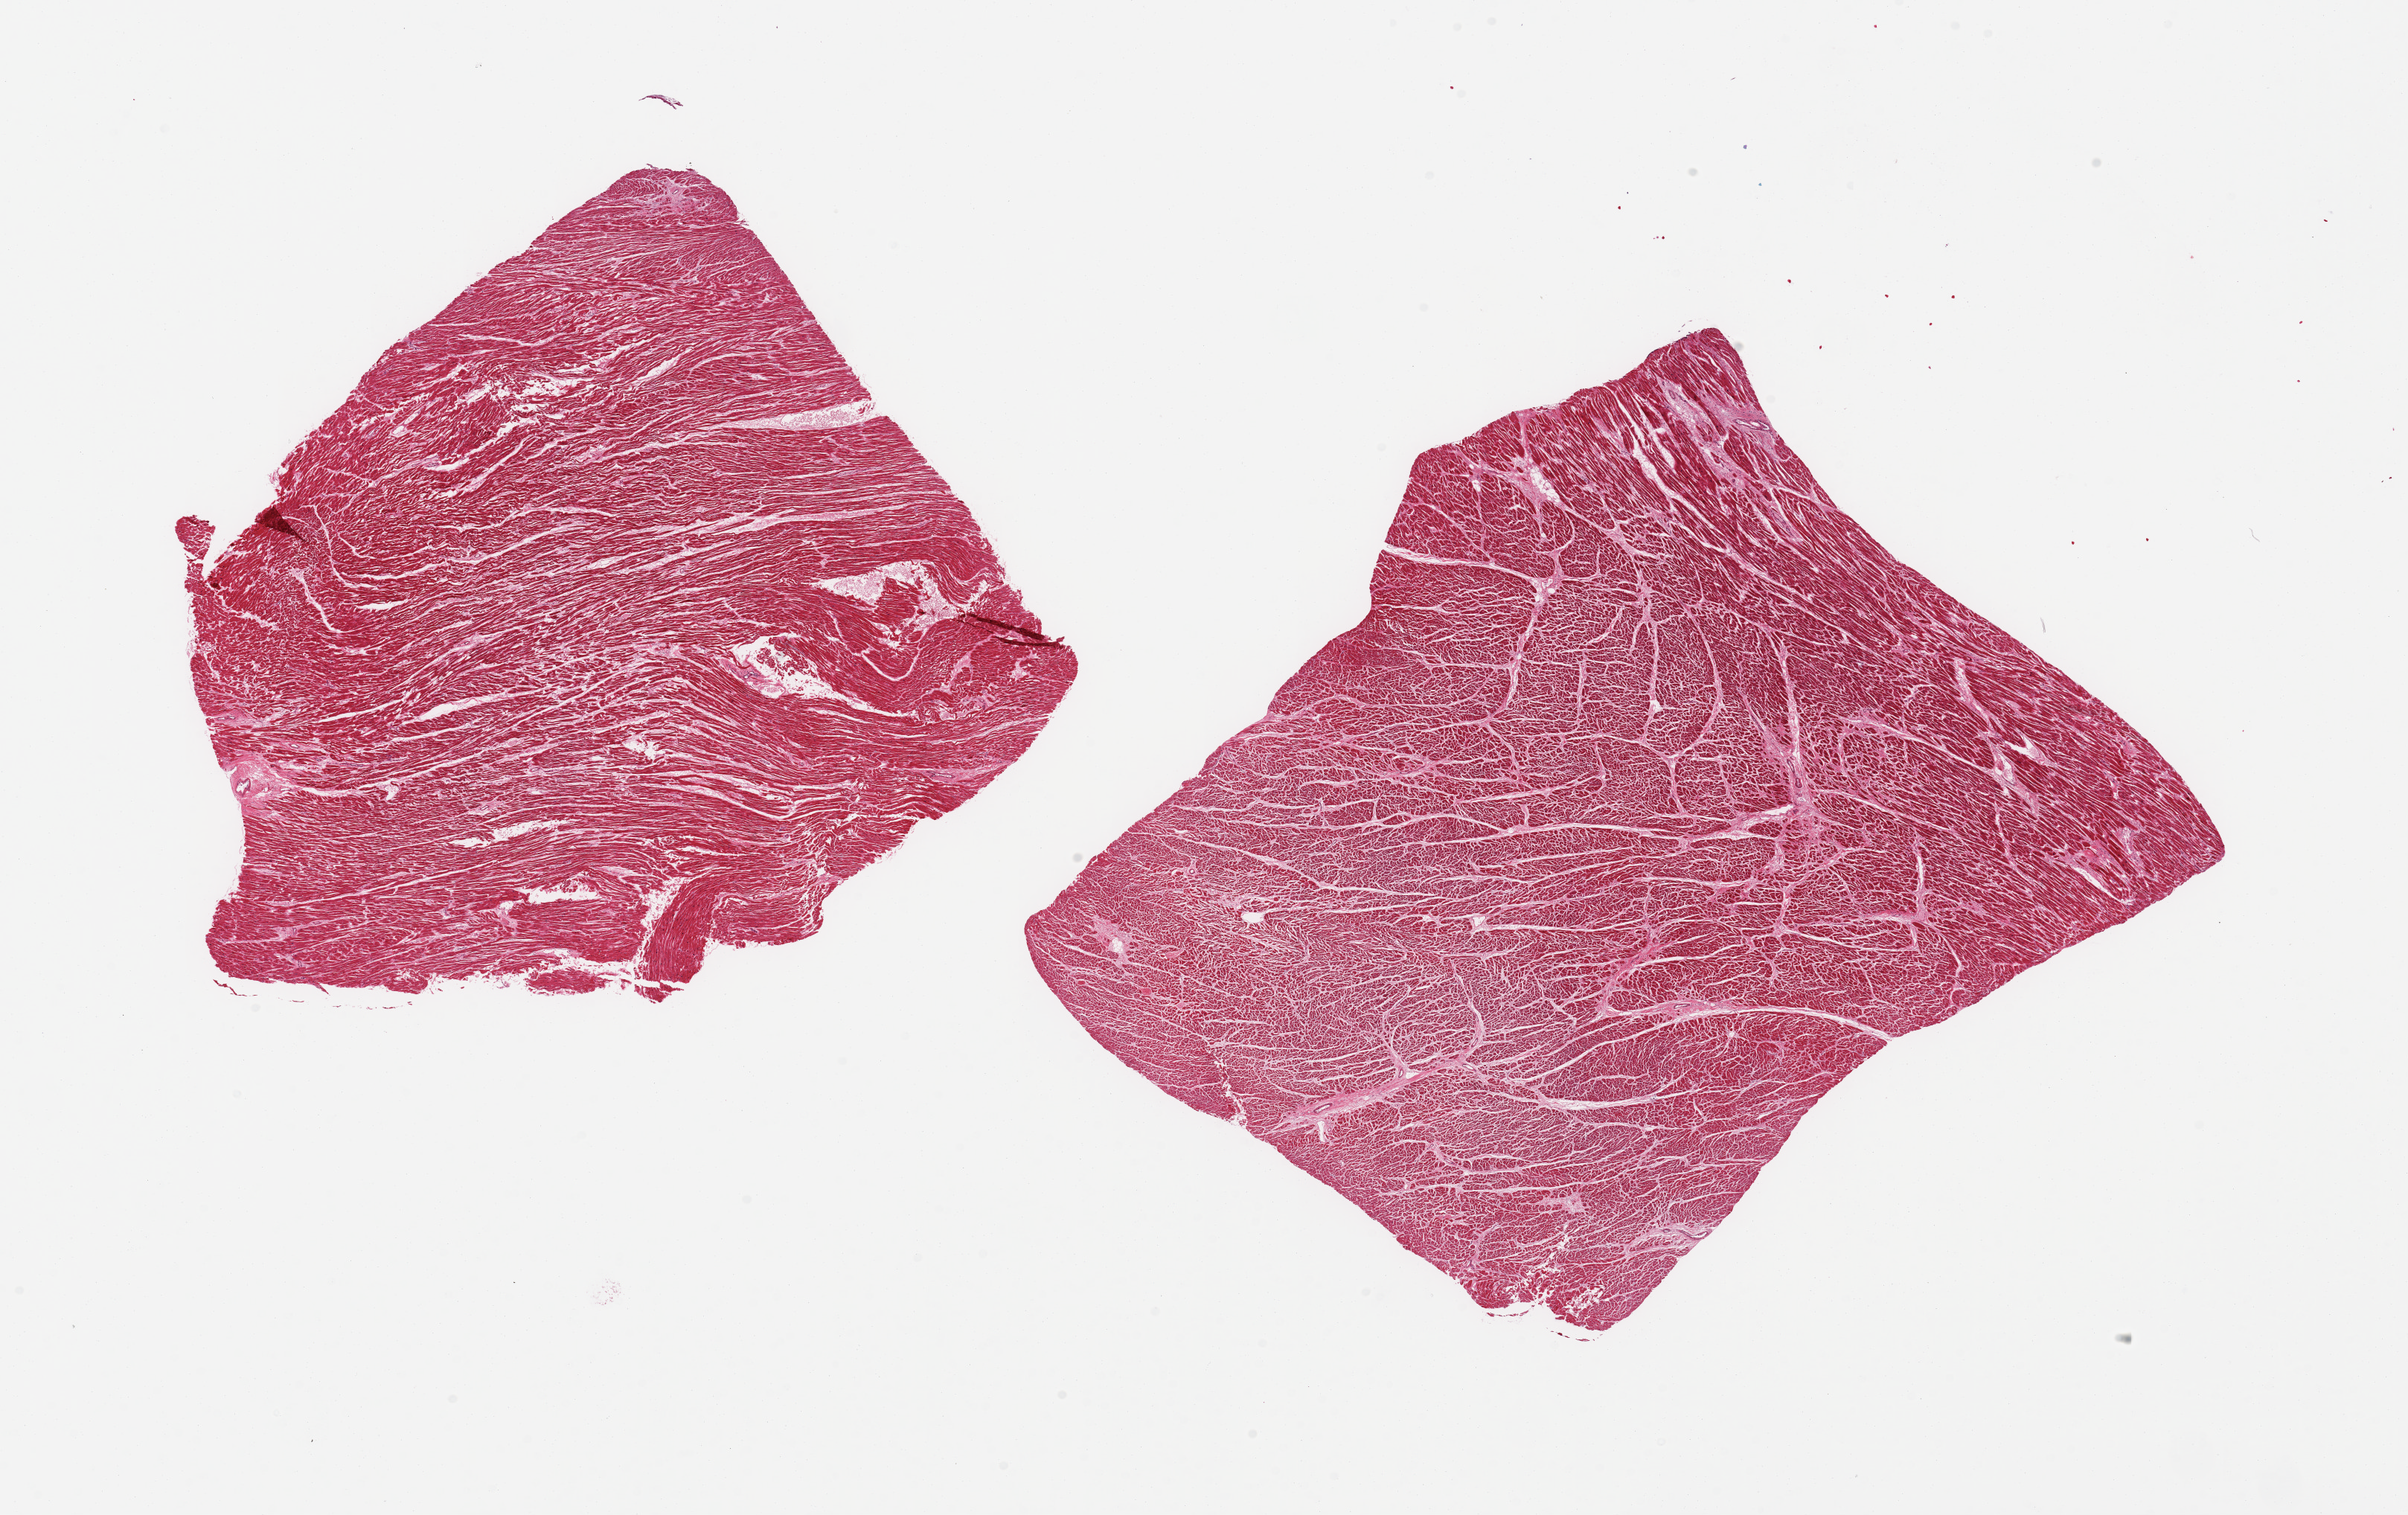
Hematoxylin and eosin (H&E) whole-slide image, brightfield, a low-resolution overview of the entire scanned area, about 25.6 x 16.1 mm. PAXgene-fixed paraffin-embedded (PFPE) section. Target tissue: heart. Donor tissue sample. Male donor.
Review note (as recorded): 2 pieces, moderate interstitial fibrosis/chronic ischemic changes.